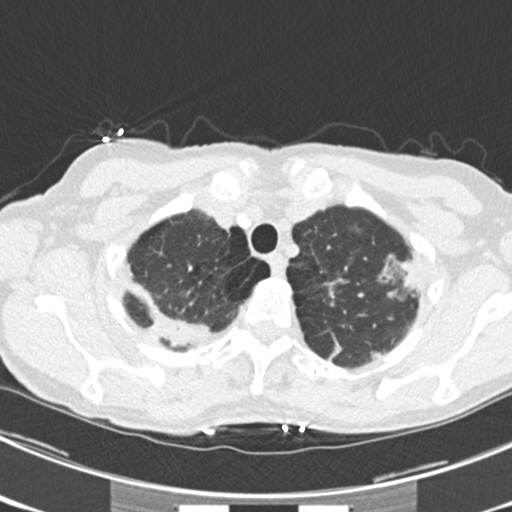
Low-dose screening chest CT, one axial slice. Position 188 of 225 along the scan axis. 120 kVp. Lung window (W 1500 / L -600 HU). 2 mm slice thickness. 512 × 512 image matrix, field of view 302 × 302 mm.
Outlined on this slice (outlined manually by an expert reader):
- lesion 1 (tumor, upper lobe of left lung): bounding box (x1, y1, x2, y2) in pixels: (397, 261, 413, 288)
- lesion 4 (tumor, upper lobe of right lung): (155, 317, 208, 346)